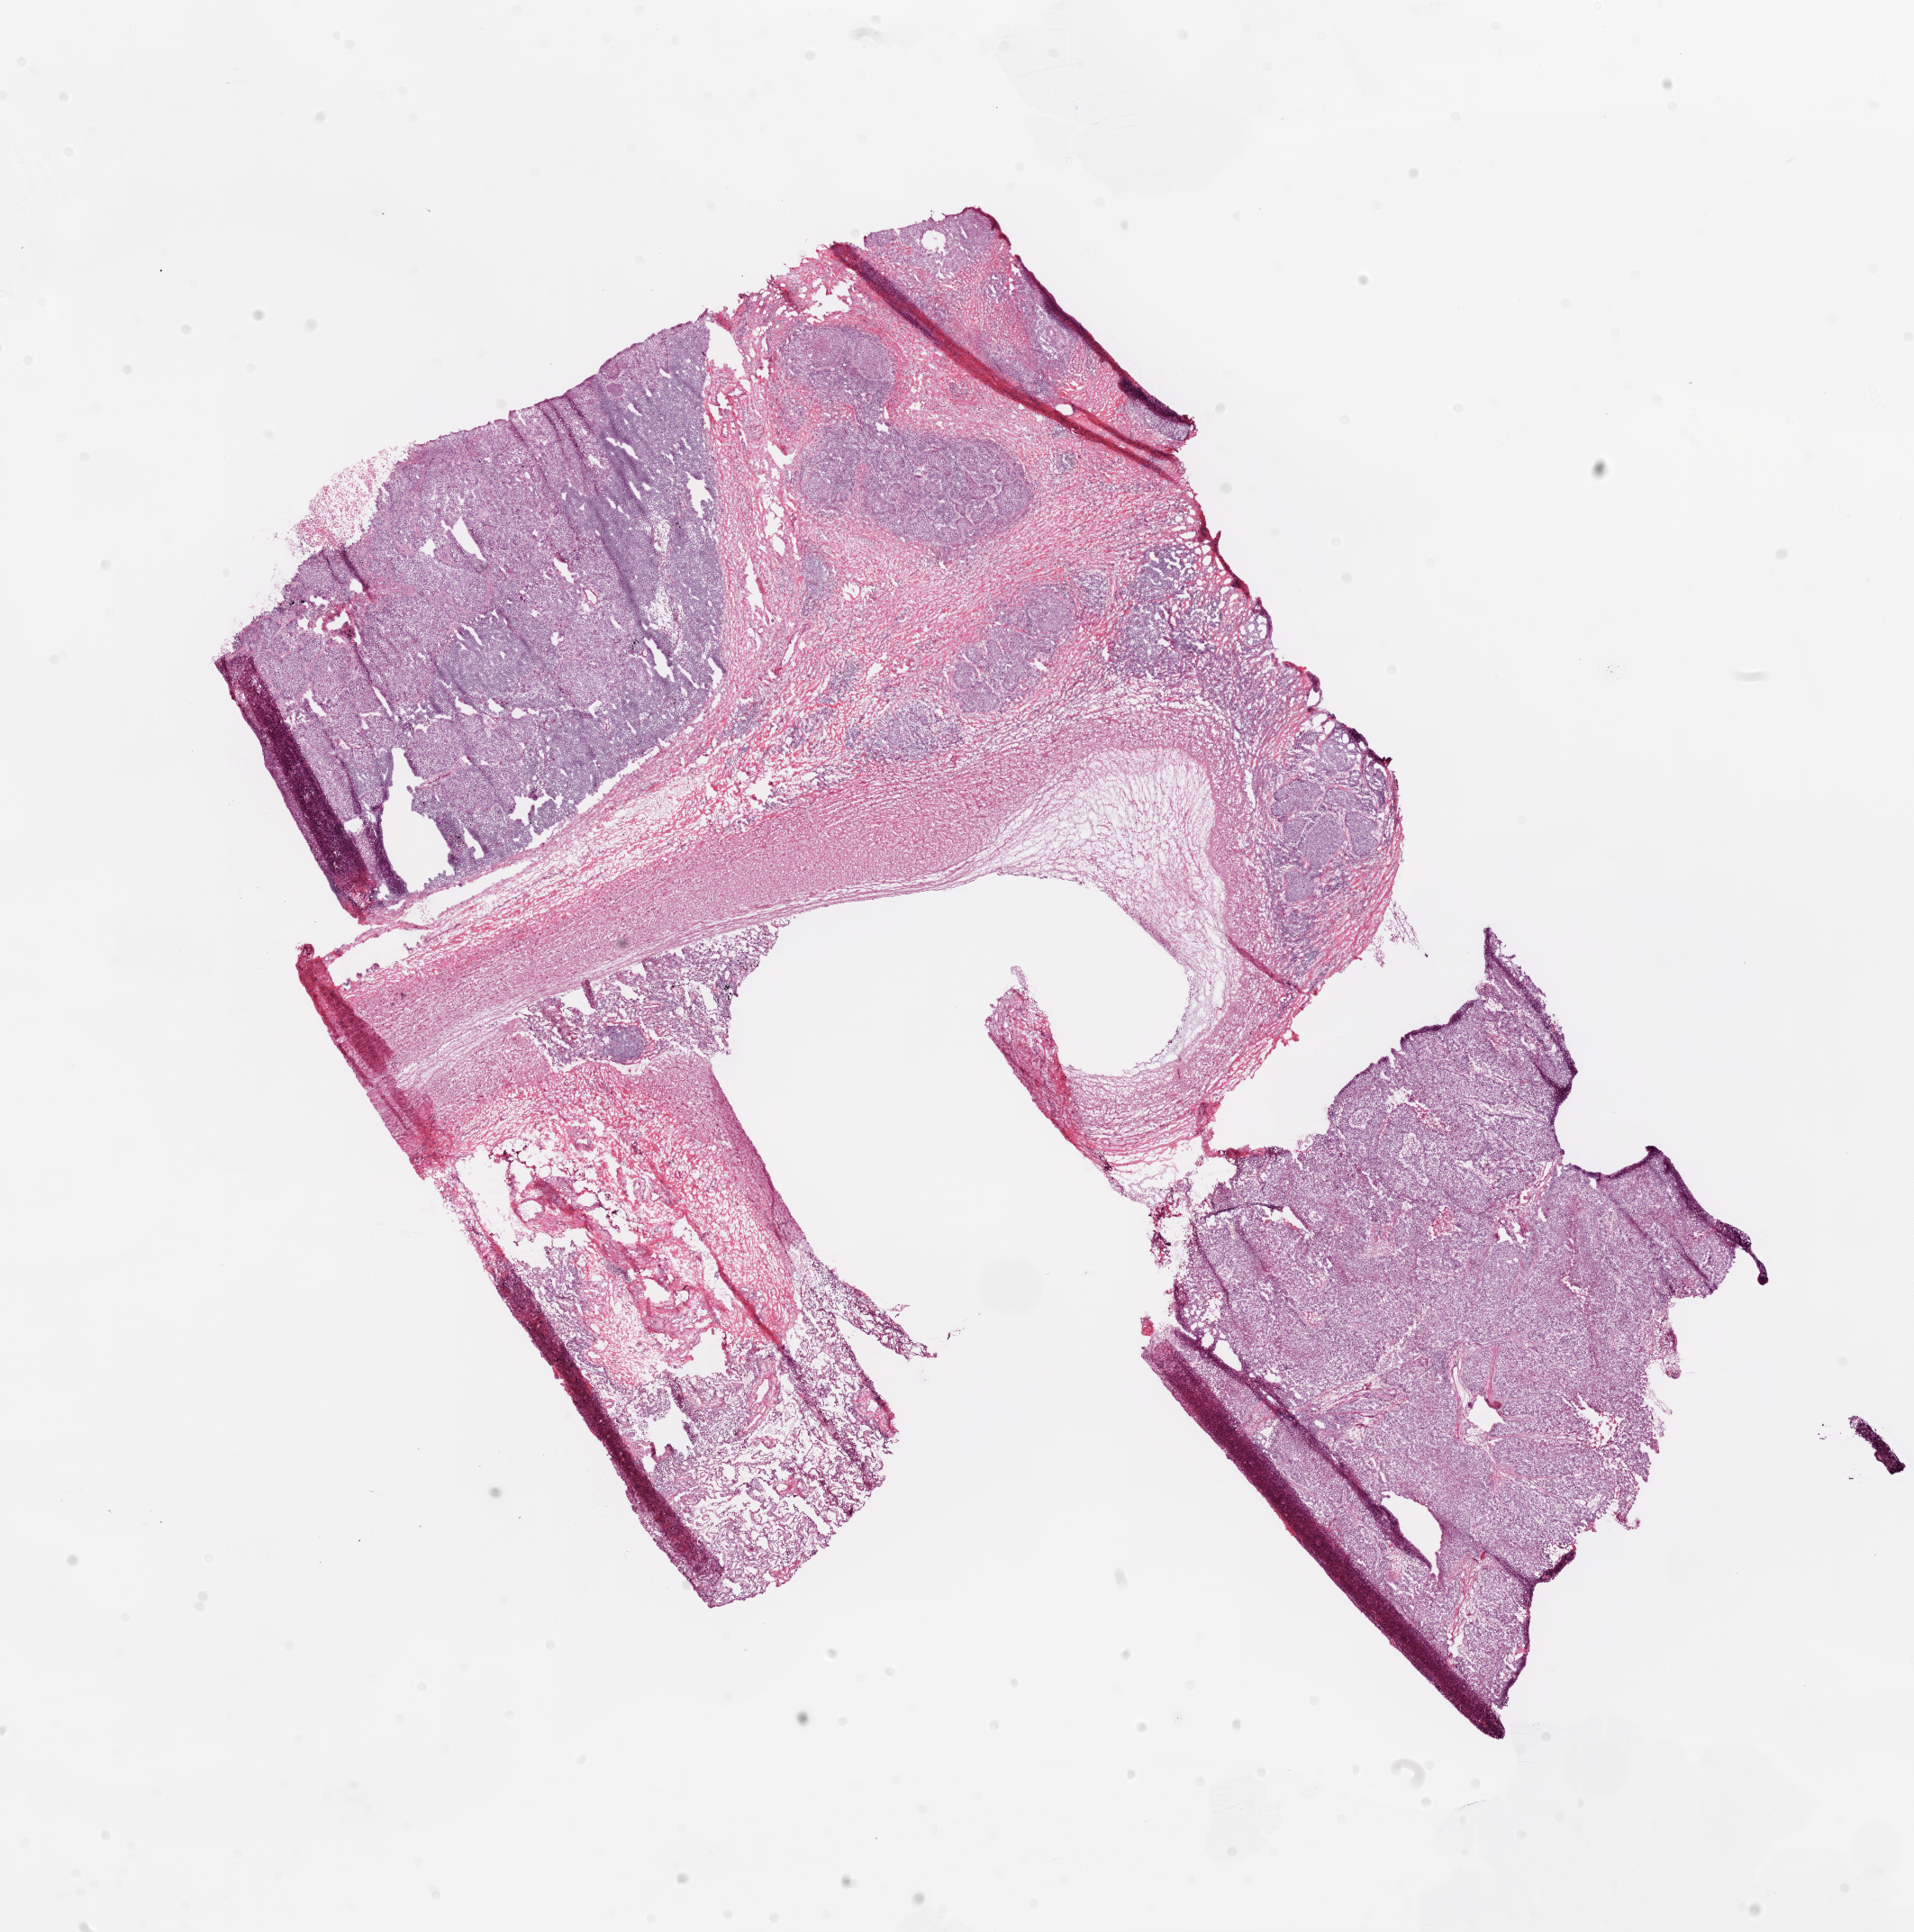
Hematoxylin and eosin (H&E) stained whole-slide image, shown as a low-resolution overview of the whole scanned area (about 17.1 x 17.2 mm, slide scanned at 20x), frozen section from the top of the tissue portion, sample: primary tumour, lung. Male patient; age at initial diagnosis 70 years. Slide review estimates, as recorded: tumour cells 80%, tumour nuclei 85%, normal cells 0%, stromal cells 15%, necrosis 0%.
Pathologic diagnosis: Squamous cell carcinoma, NOS. AJCC pathologic stage: IIB.